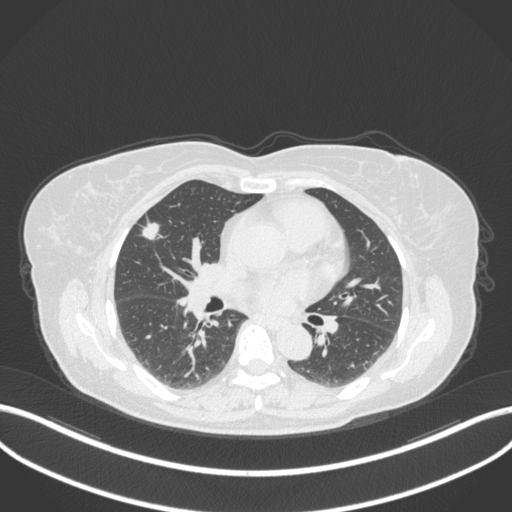
Chest CT, one axial slice; position 176 of 310 along the scan axis; reconstruction kernel B31f; 120 kVp; lung window (W 1500 / L -600 HU); 1 mm slice thickness; 512 × 512 image matrix, field of view 400 × 400 mm. Female patient, age 55 years. Case-level facts recorded for this patient, not image findings: clinical TNM (as recorded): T1b N0 M0; histopathological grade: G2.
Structures marked on this image (rectangle marked by the reading radiologist):
- lung tumour (recorded histology: adenocarcinoma): bounding box [x1, y1, x2, y2] px = [140, 218, 164, 243]